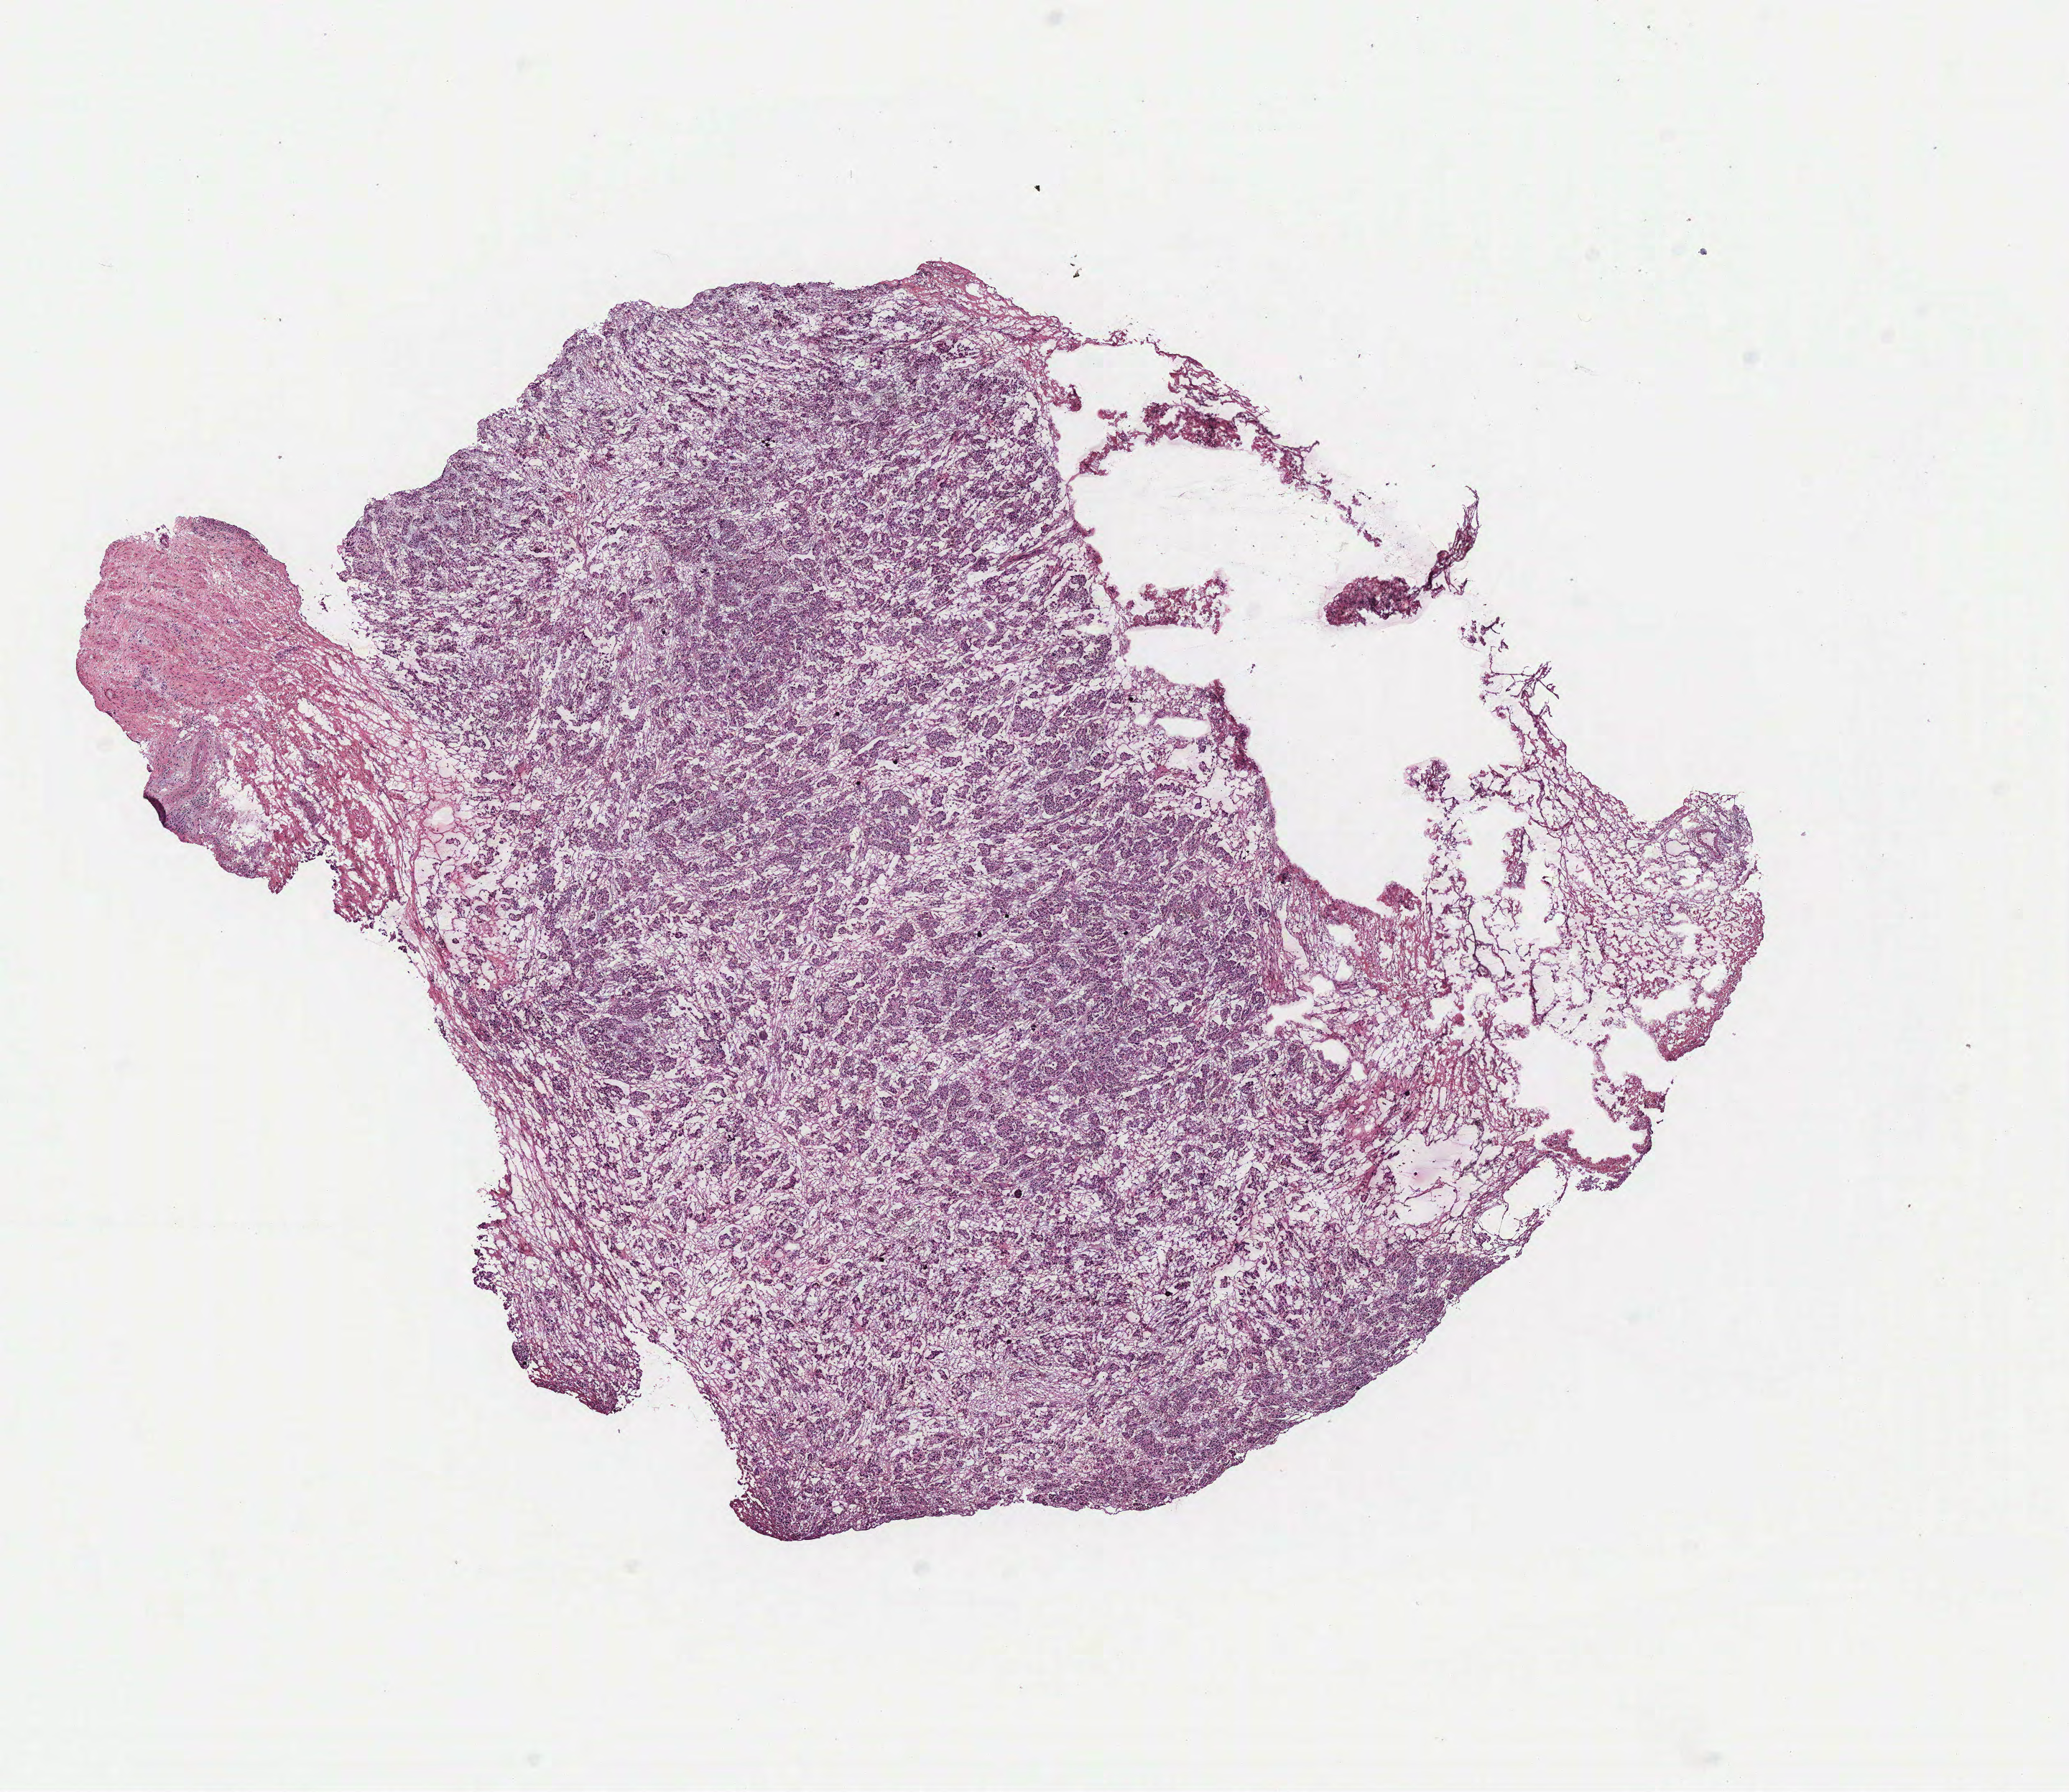
Hematoxylin and eosin (H&E) stained whole-slide image — low-resolution overview of the scanned area, about 11.5 x 10.0 mm, tumour tissue sample, ovary. 69-year-old female patient.
Histologic diagnosis: Serous adenocarcinoma, NOS. Primary tumour site (as recorded): ovary.